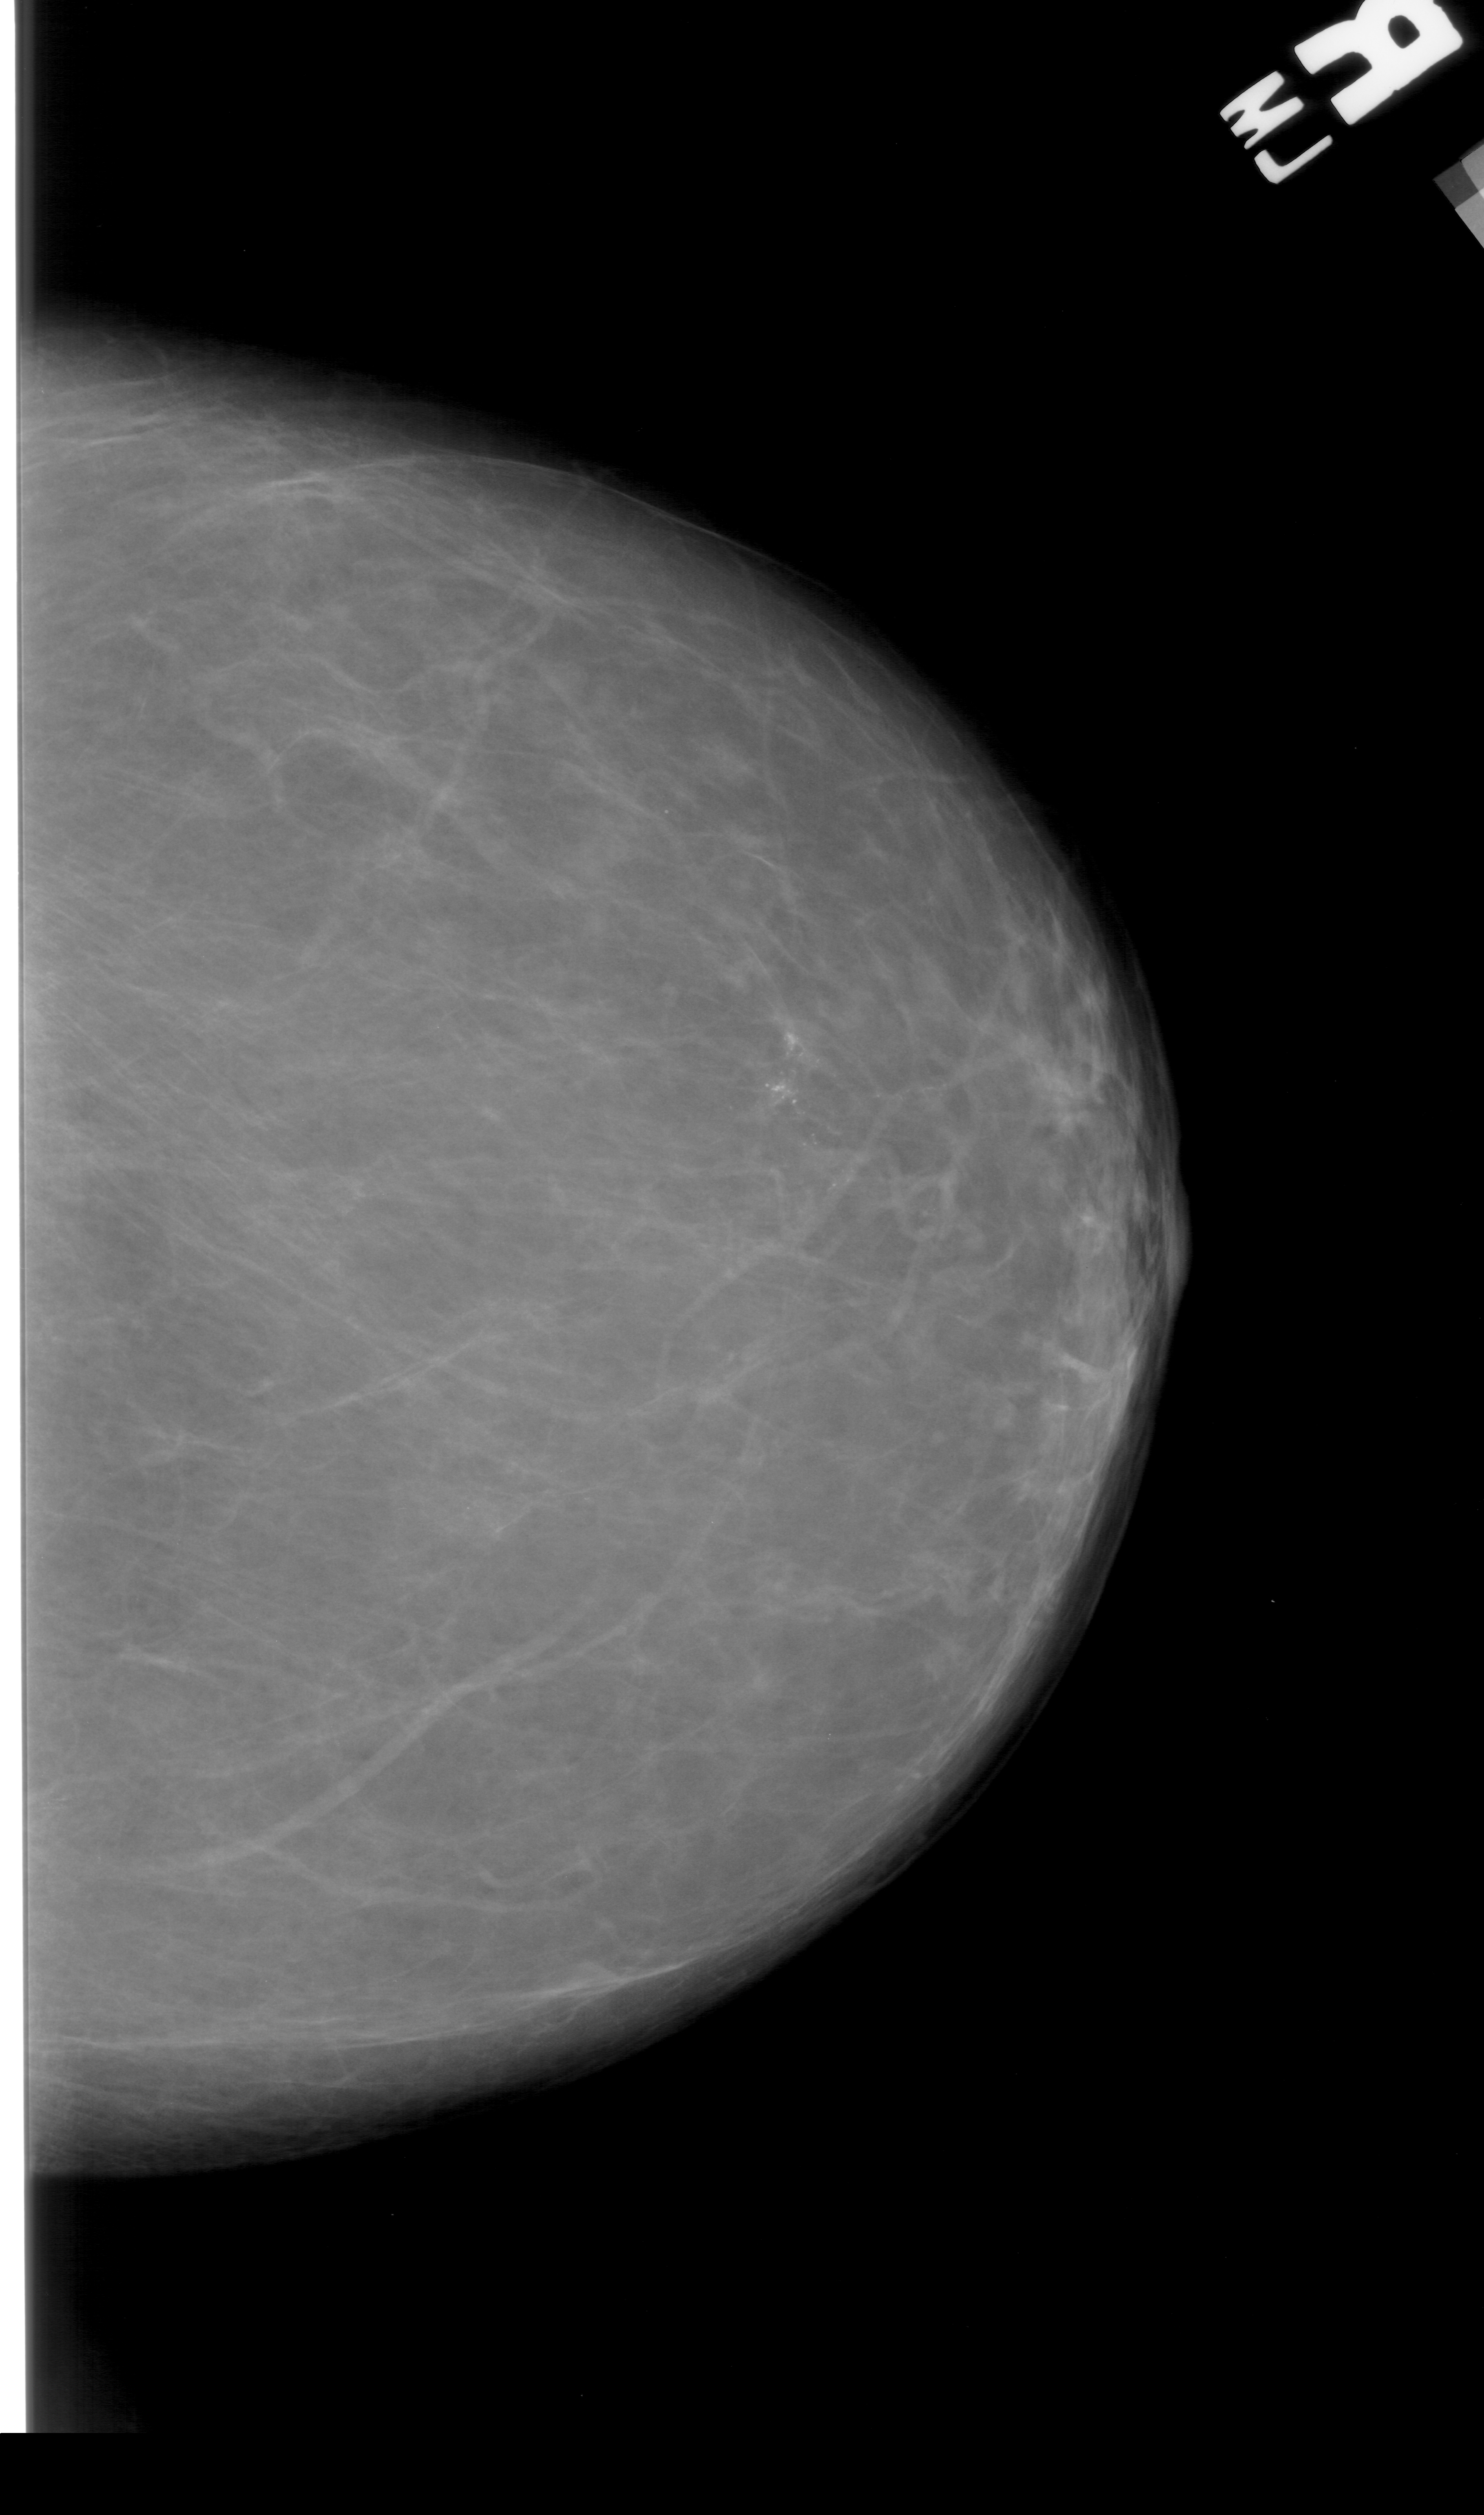
Digitized screen-film mammogram. Right breast. Craniocaudal (CC) view. Breast composition: scattered fibroglandular densities (BI-RADS density category 2 of 4). 1484 × 2515 image matrix.
Marked abnormalities (boxes around the expert regions of interest):
- calcifications, morphology pleomorphic, distribution segmental; BI-RADS assessment category 4; pathology (as recorded): malignant: box from (x=727, y=997) to (x=944, y=1215) px